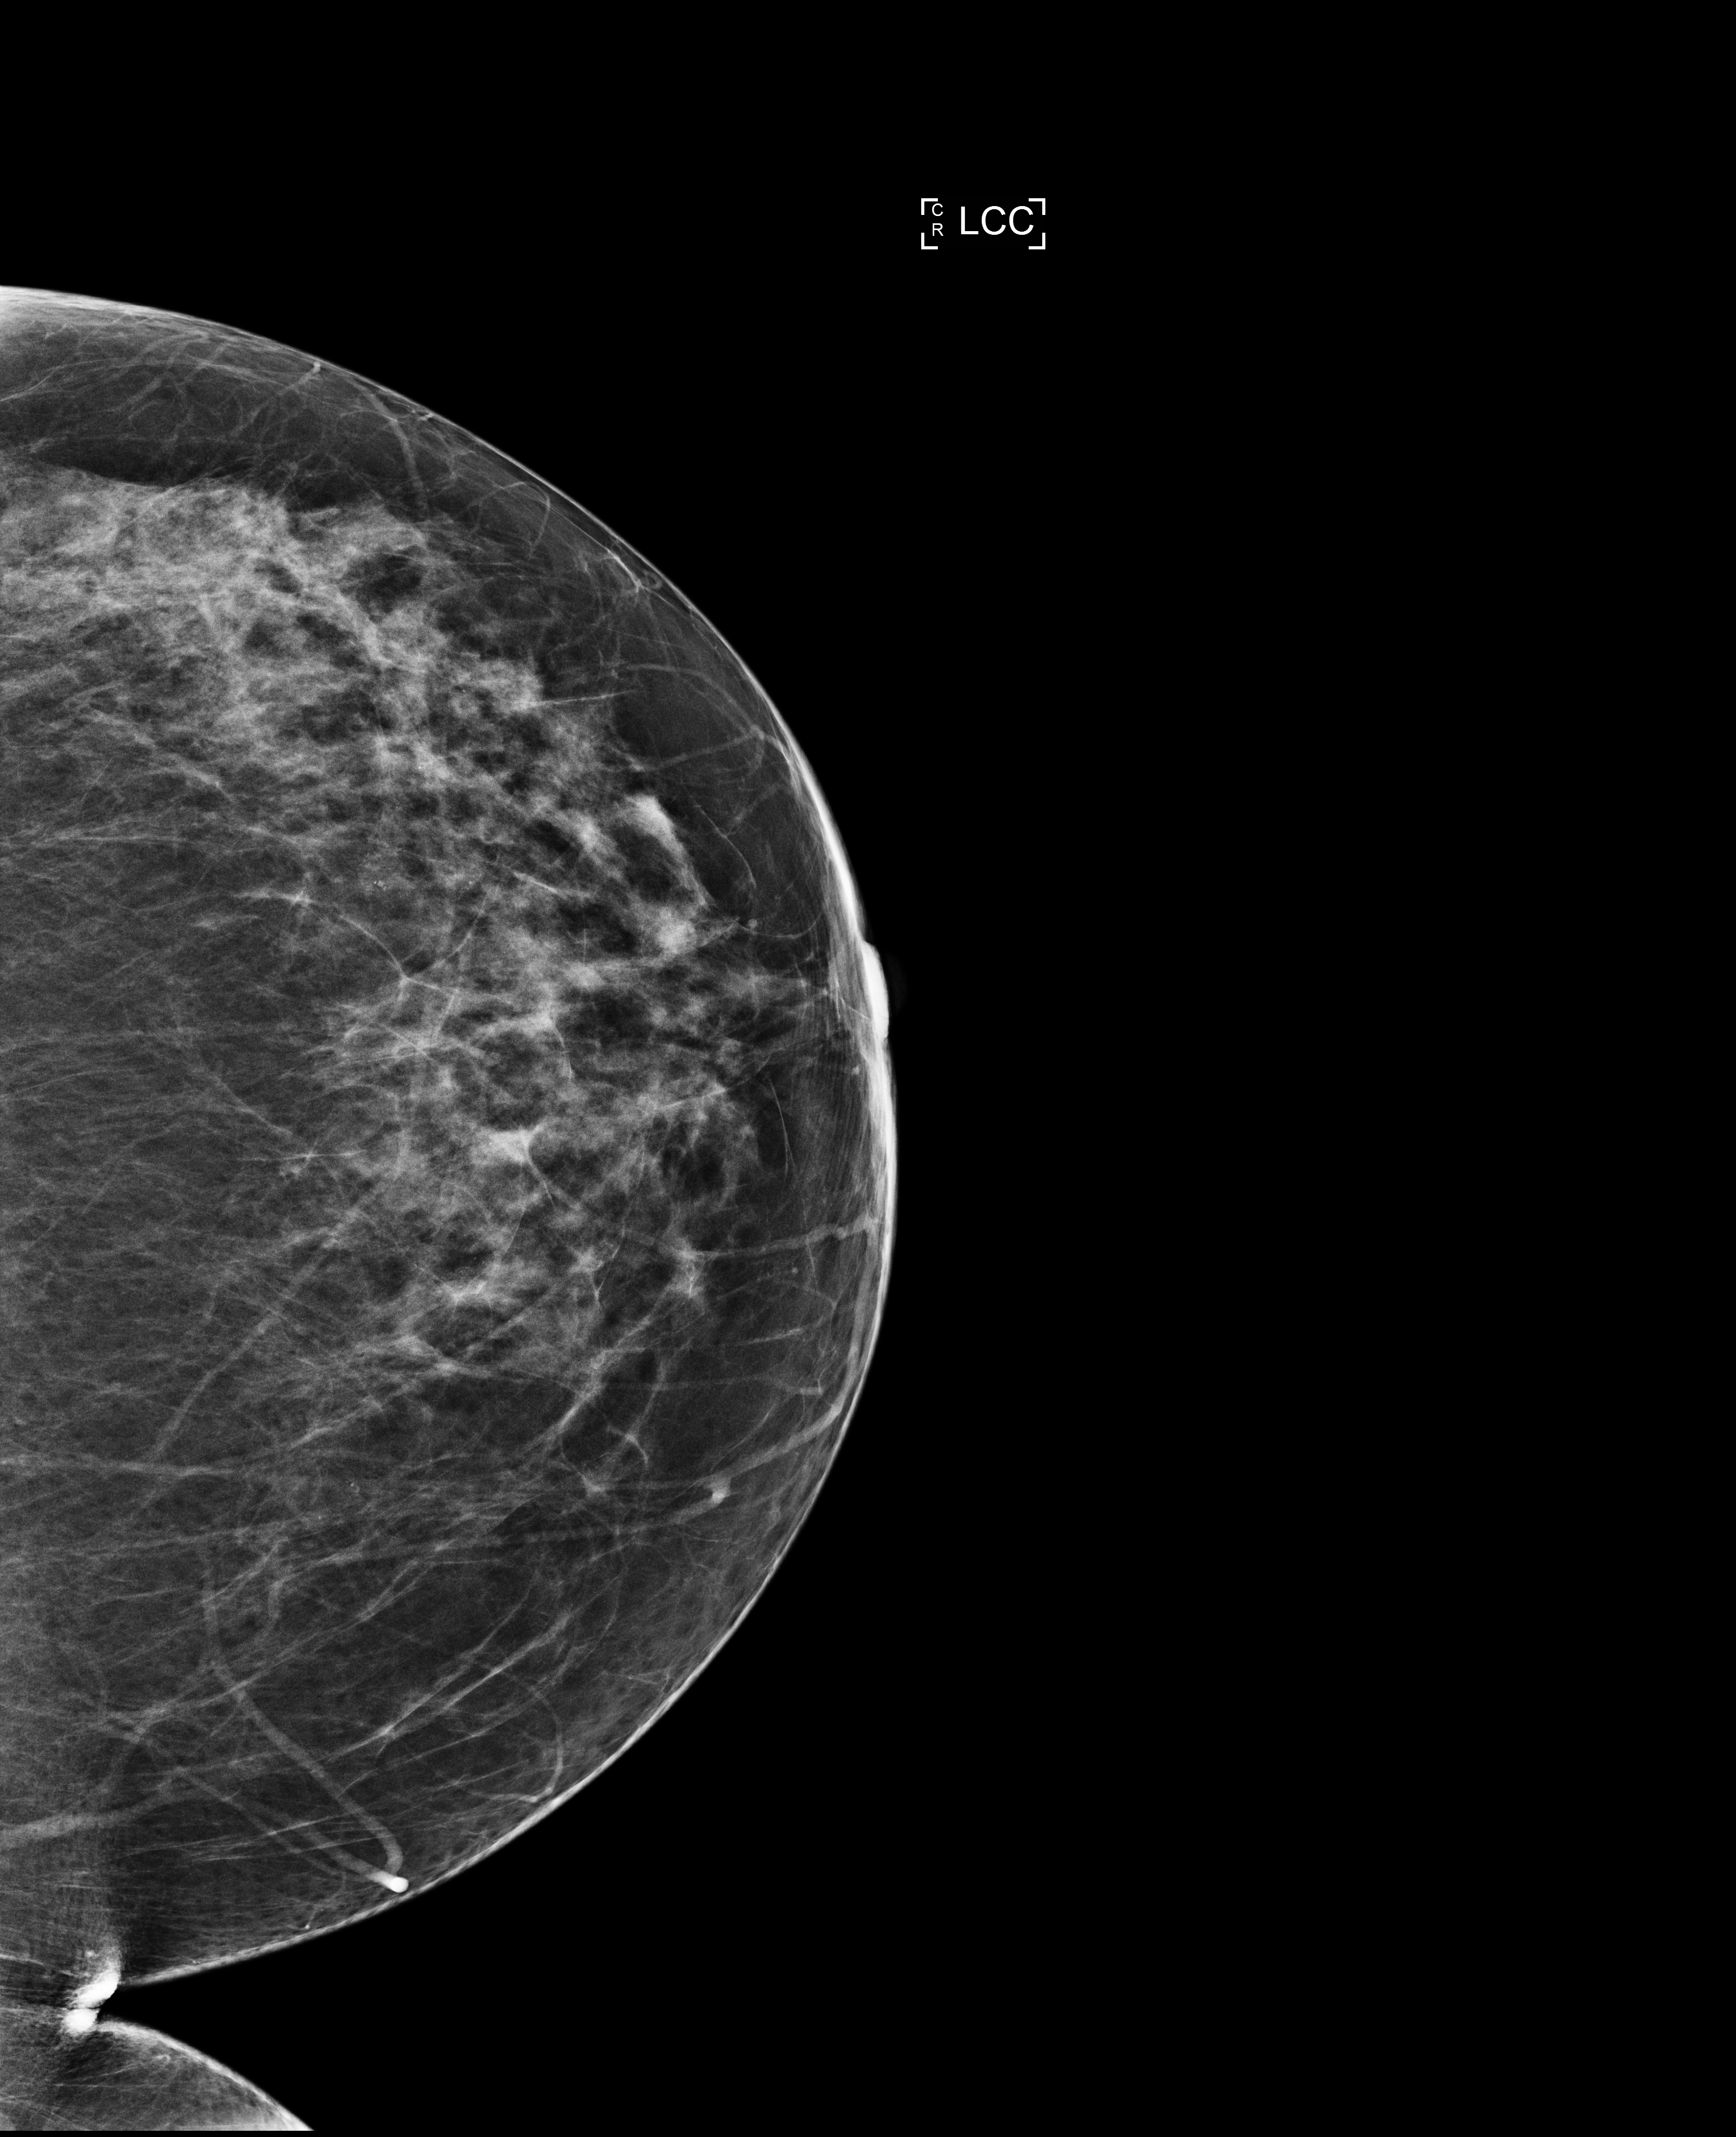
Annual screening mammography examination. Female patient, age 58 years.
Image type: full-field digital mammogram. Breast: left. Projection: cranio-caudal projection.